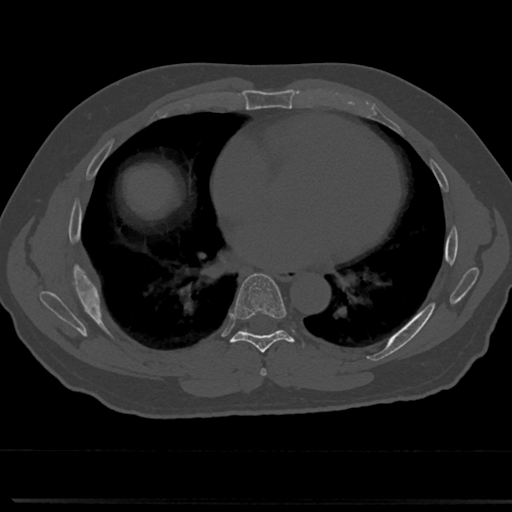
CT including the spine, one axial slice. Position 401 of 817 along the scan axis. 120 kVp. Bone window (W 1800 / L 400 HU). 0.5 mm slice thickness. 512 × 512 image matrix, field of view 355 × 355 mm. Male patient, age 61 years. From the clinical record (not read from this slice): primary cancer: prostate.
Outlined on this slice (semi-automatically segmented with operator editing):
- T6 vertebra: box from (x=261, y=340) to (x=319, y=376) px
- T7 vertebra: (x=214, y=275)–(x=310, y=358)